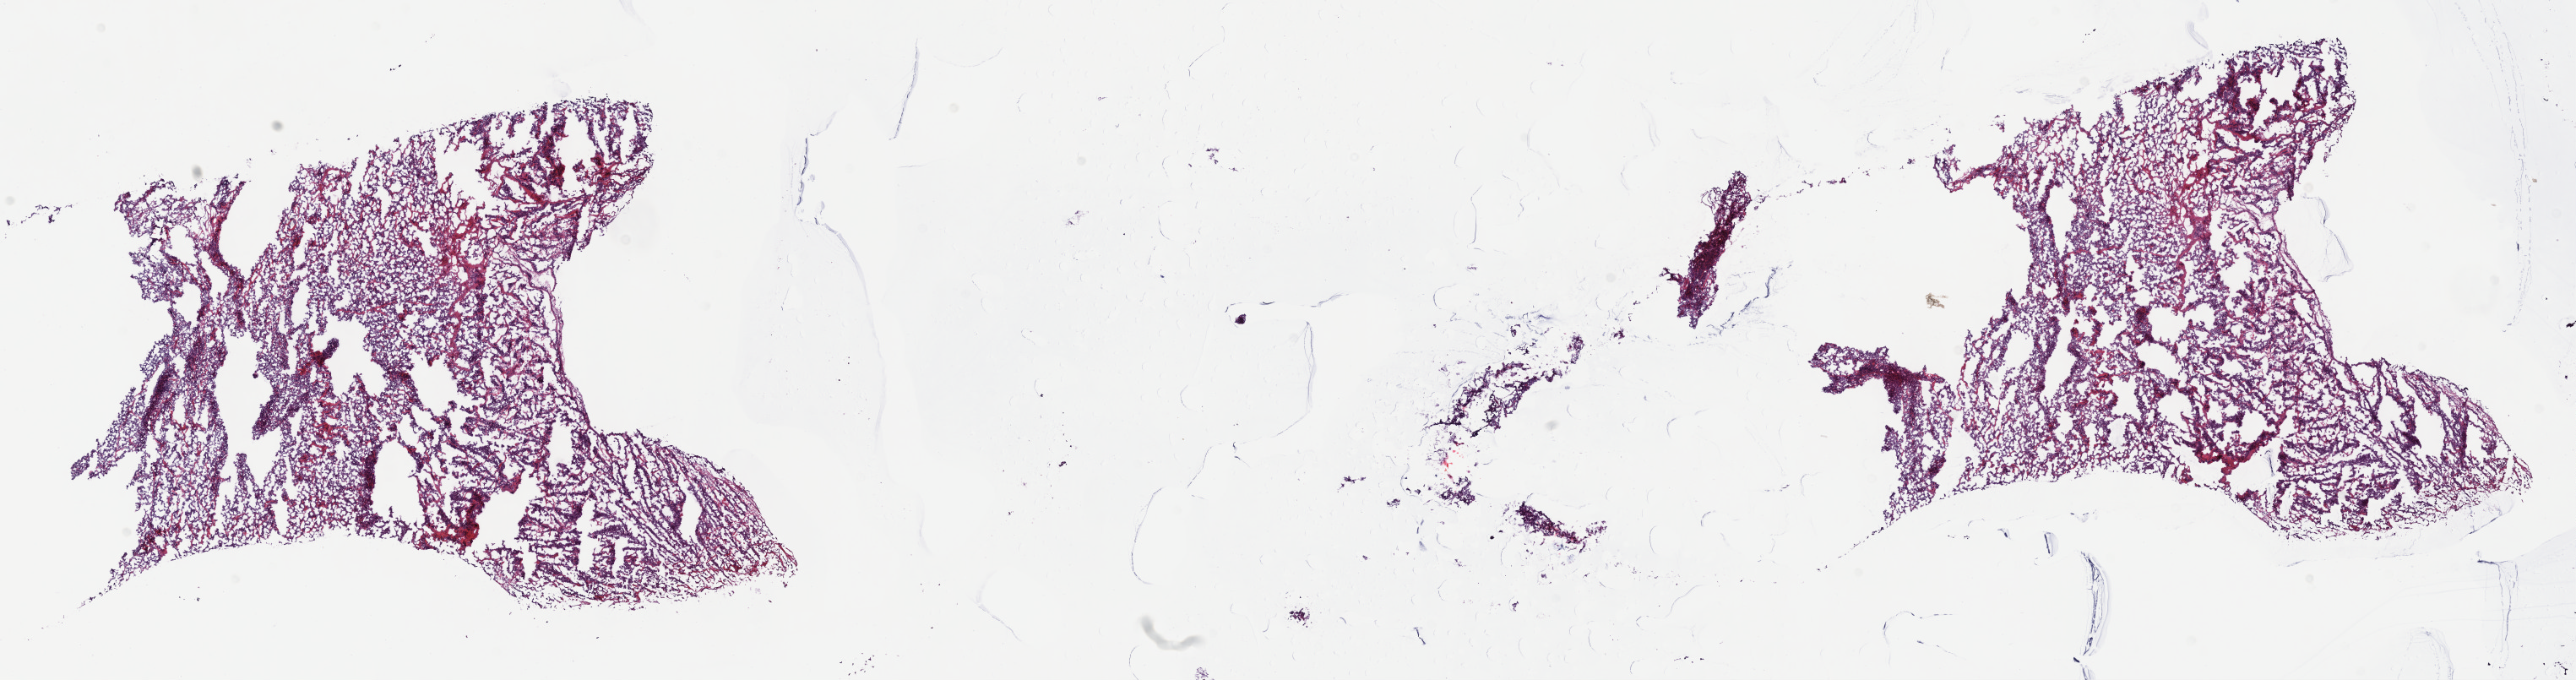
H&E whole-slide image, a low-resolution overview of the entire scanned area, about 24.7 x 6.5 mm (from a 40x scan); frozen section from the top of the tissue portion; mesothelium, primary tumour sample. Male patient; age at initial diagnosis 71 years. Composition of this section per pathologist review: tumour cells 60%, tumour nuclei 60%, normal cells 20%, stromal cells 20%, necrosis 0%. Inflammatory infiltration, as recorded: lymphocyte infiltration 70%, monocyte infiltration 10%, neutrophil infiltration 10%.
- pathologic diagnosis: Epithelioid mesothelioma, malignant (pleura, NOS)
- AJCC pathologic stage: III (6th edition)